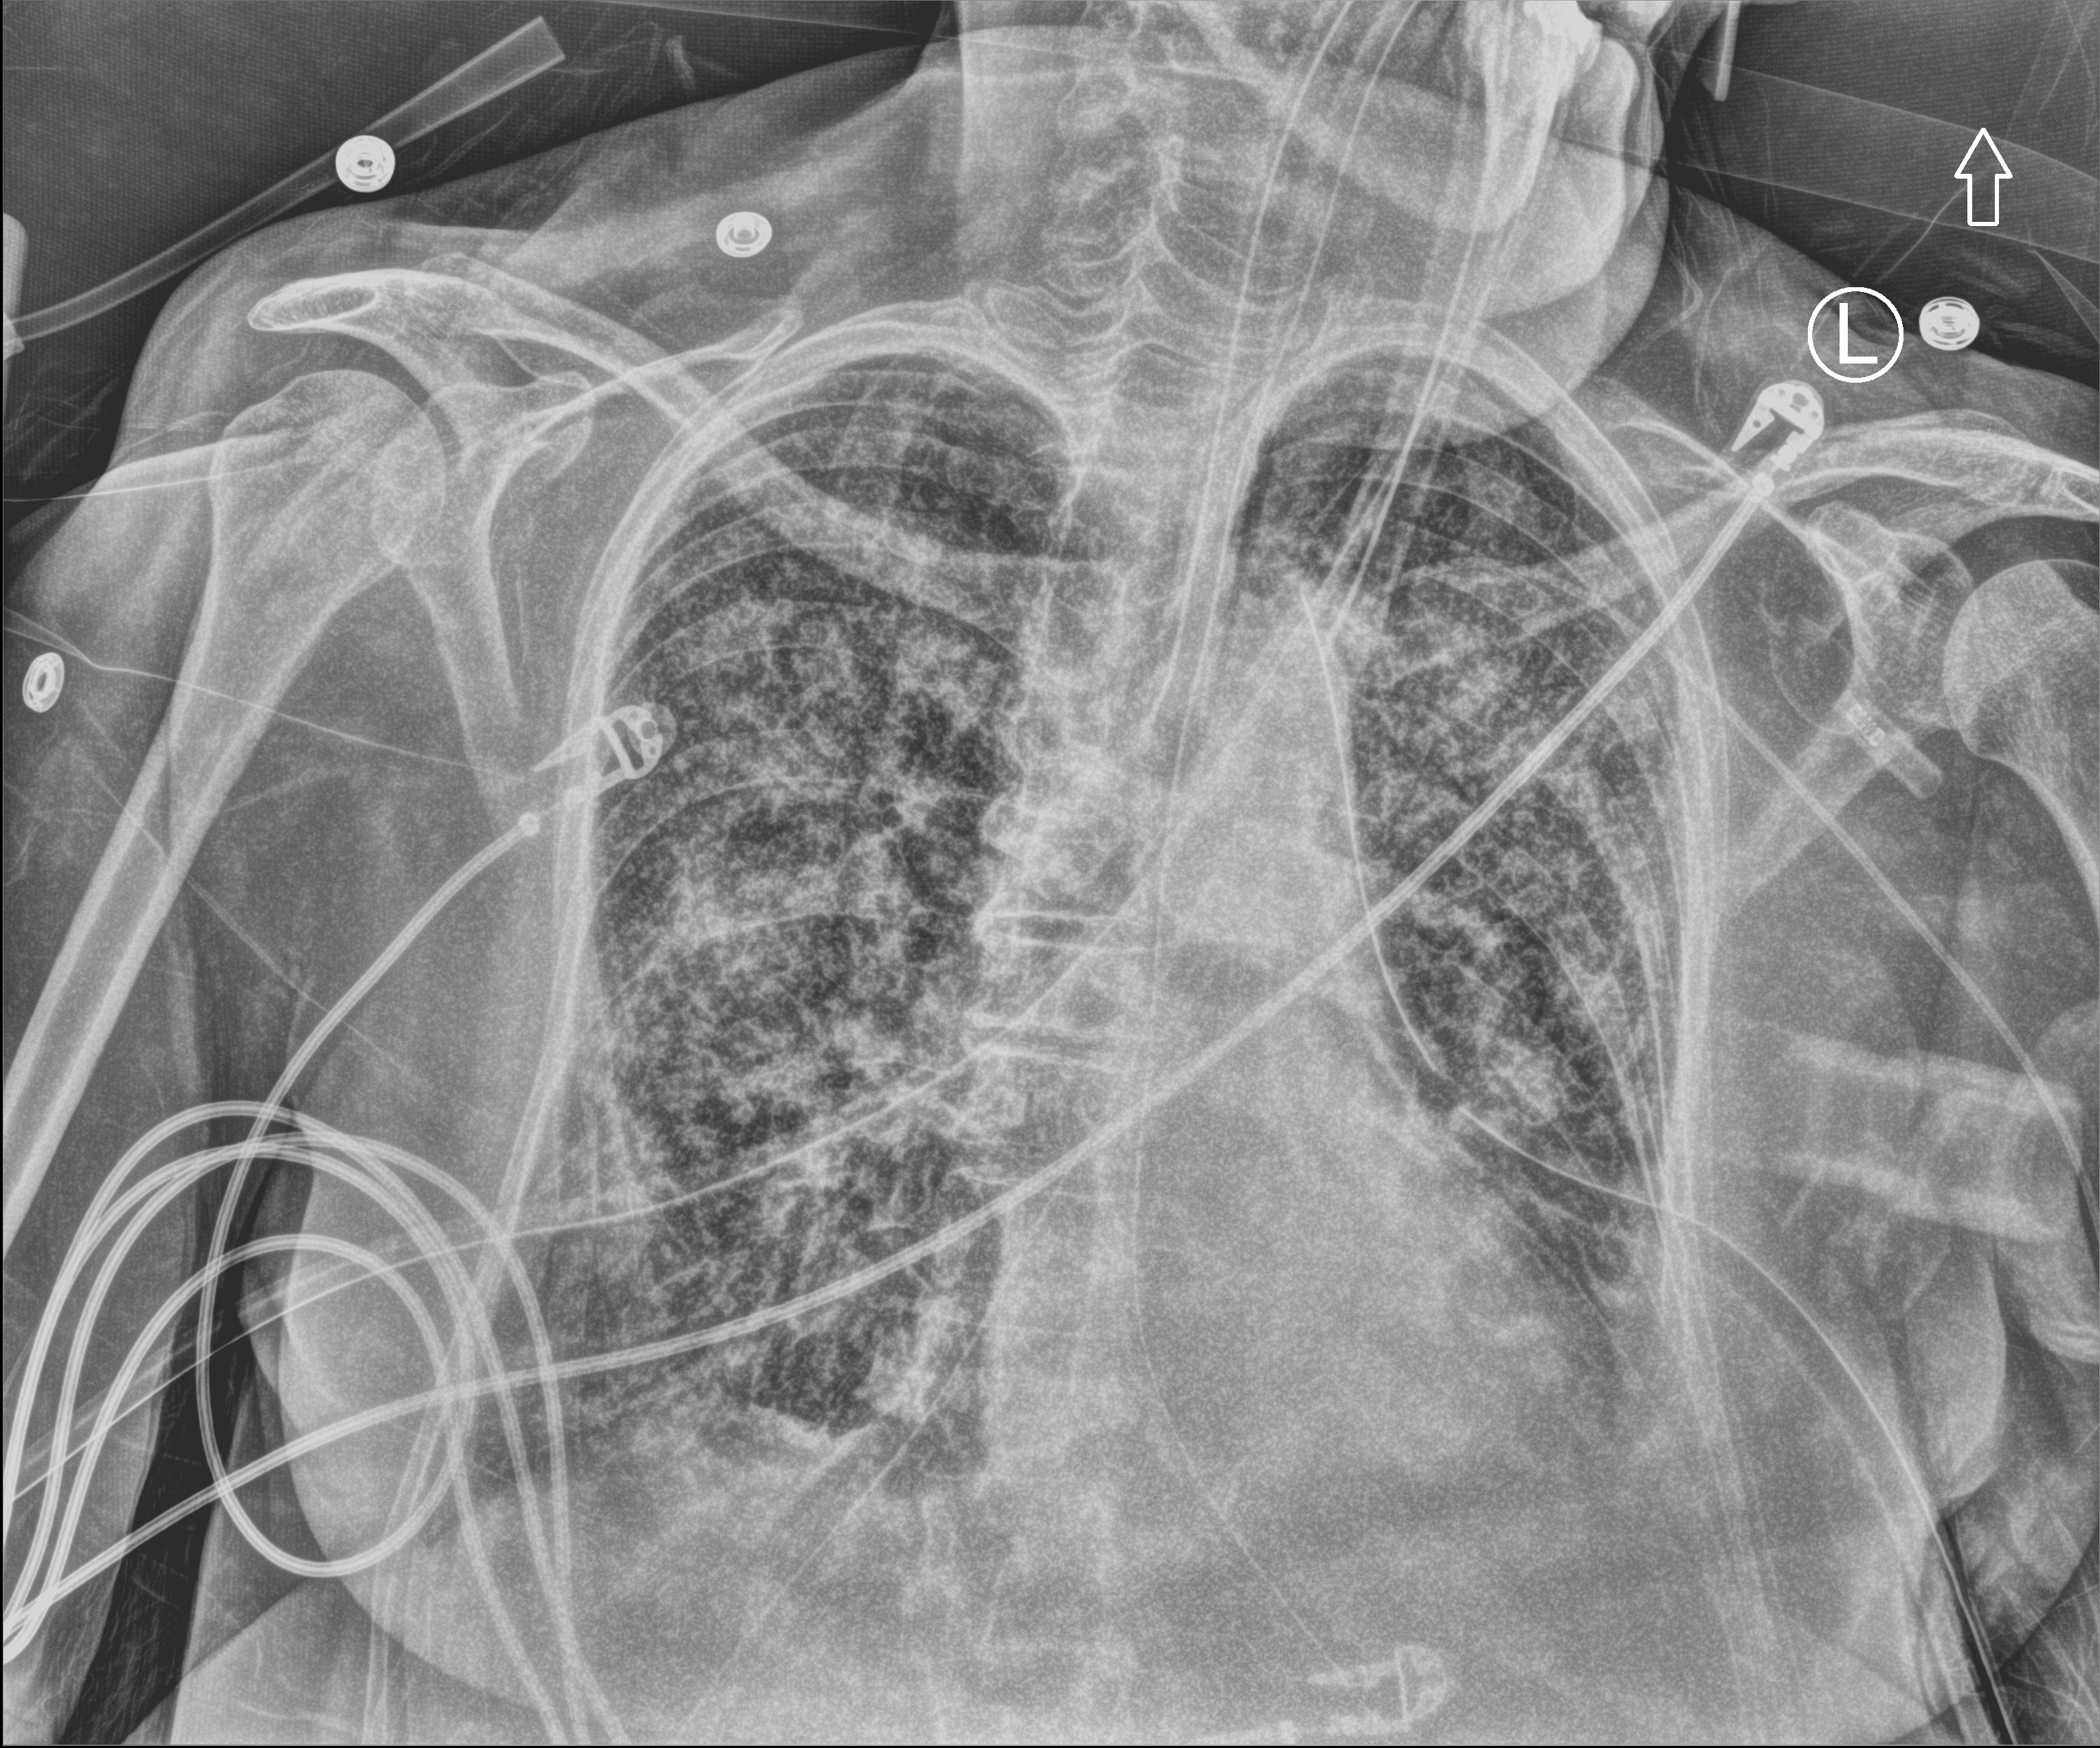
Chest X-ray (portable); anteroposterior (AP) projection. Female patient hospitalised with COVID-19, age 75–90 years.
From the hospital-stay record, not from the radiograph (when in the stay this image was taken is not recorded):
- admitted to intensive care during this hospital stay: yes
- mechanically ventilated during this hospital stay: yes
- diabetes (admission record): no